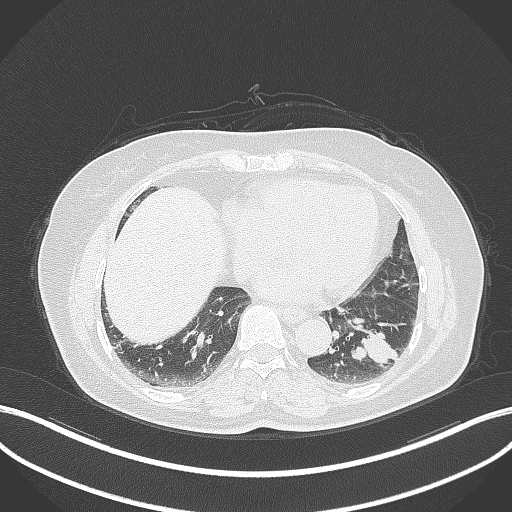
Chest CT, one axial slice; slice 128 of 311 in the series (ordered by position); 120 kVp; lung window (W 1500 / L -600 HU); 1 mm slice thickness; 512 × 512 image matrix, field of view 400 × 400 mm. Patient: female, 59 years. Case-level facts recorded for this patient, not image findings: clinical TNM (as recorded): T2a N0 M0; histopathological grade: G2-3.
Annotated regions visible in this slice (rectangle marked by the reading radiologist):
- lung tumour (recorded histology: adenocarcinoma): bounding box <348,323,401,369> (left, top, right, bottom; pixels)